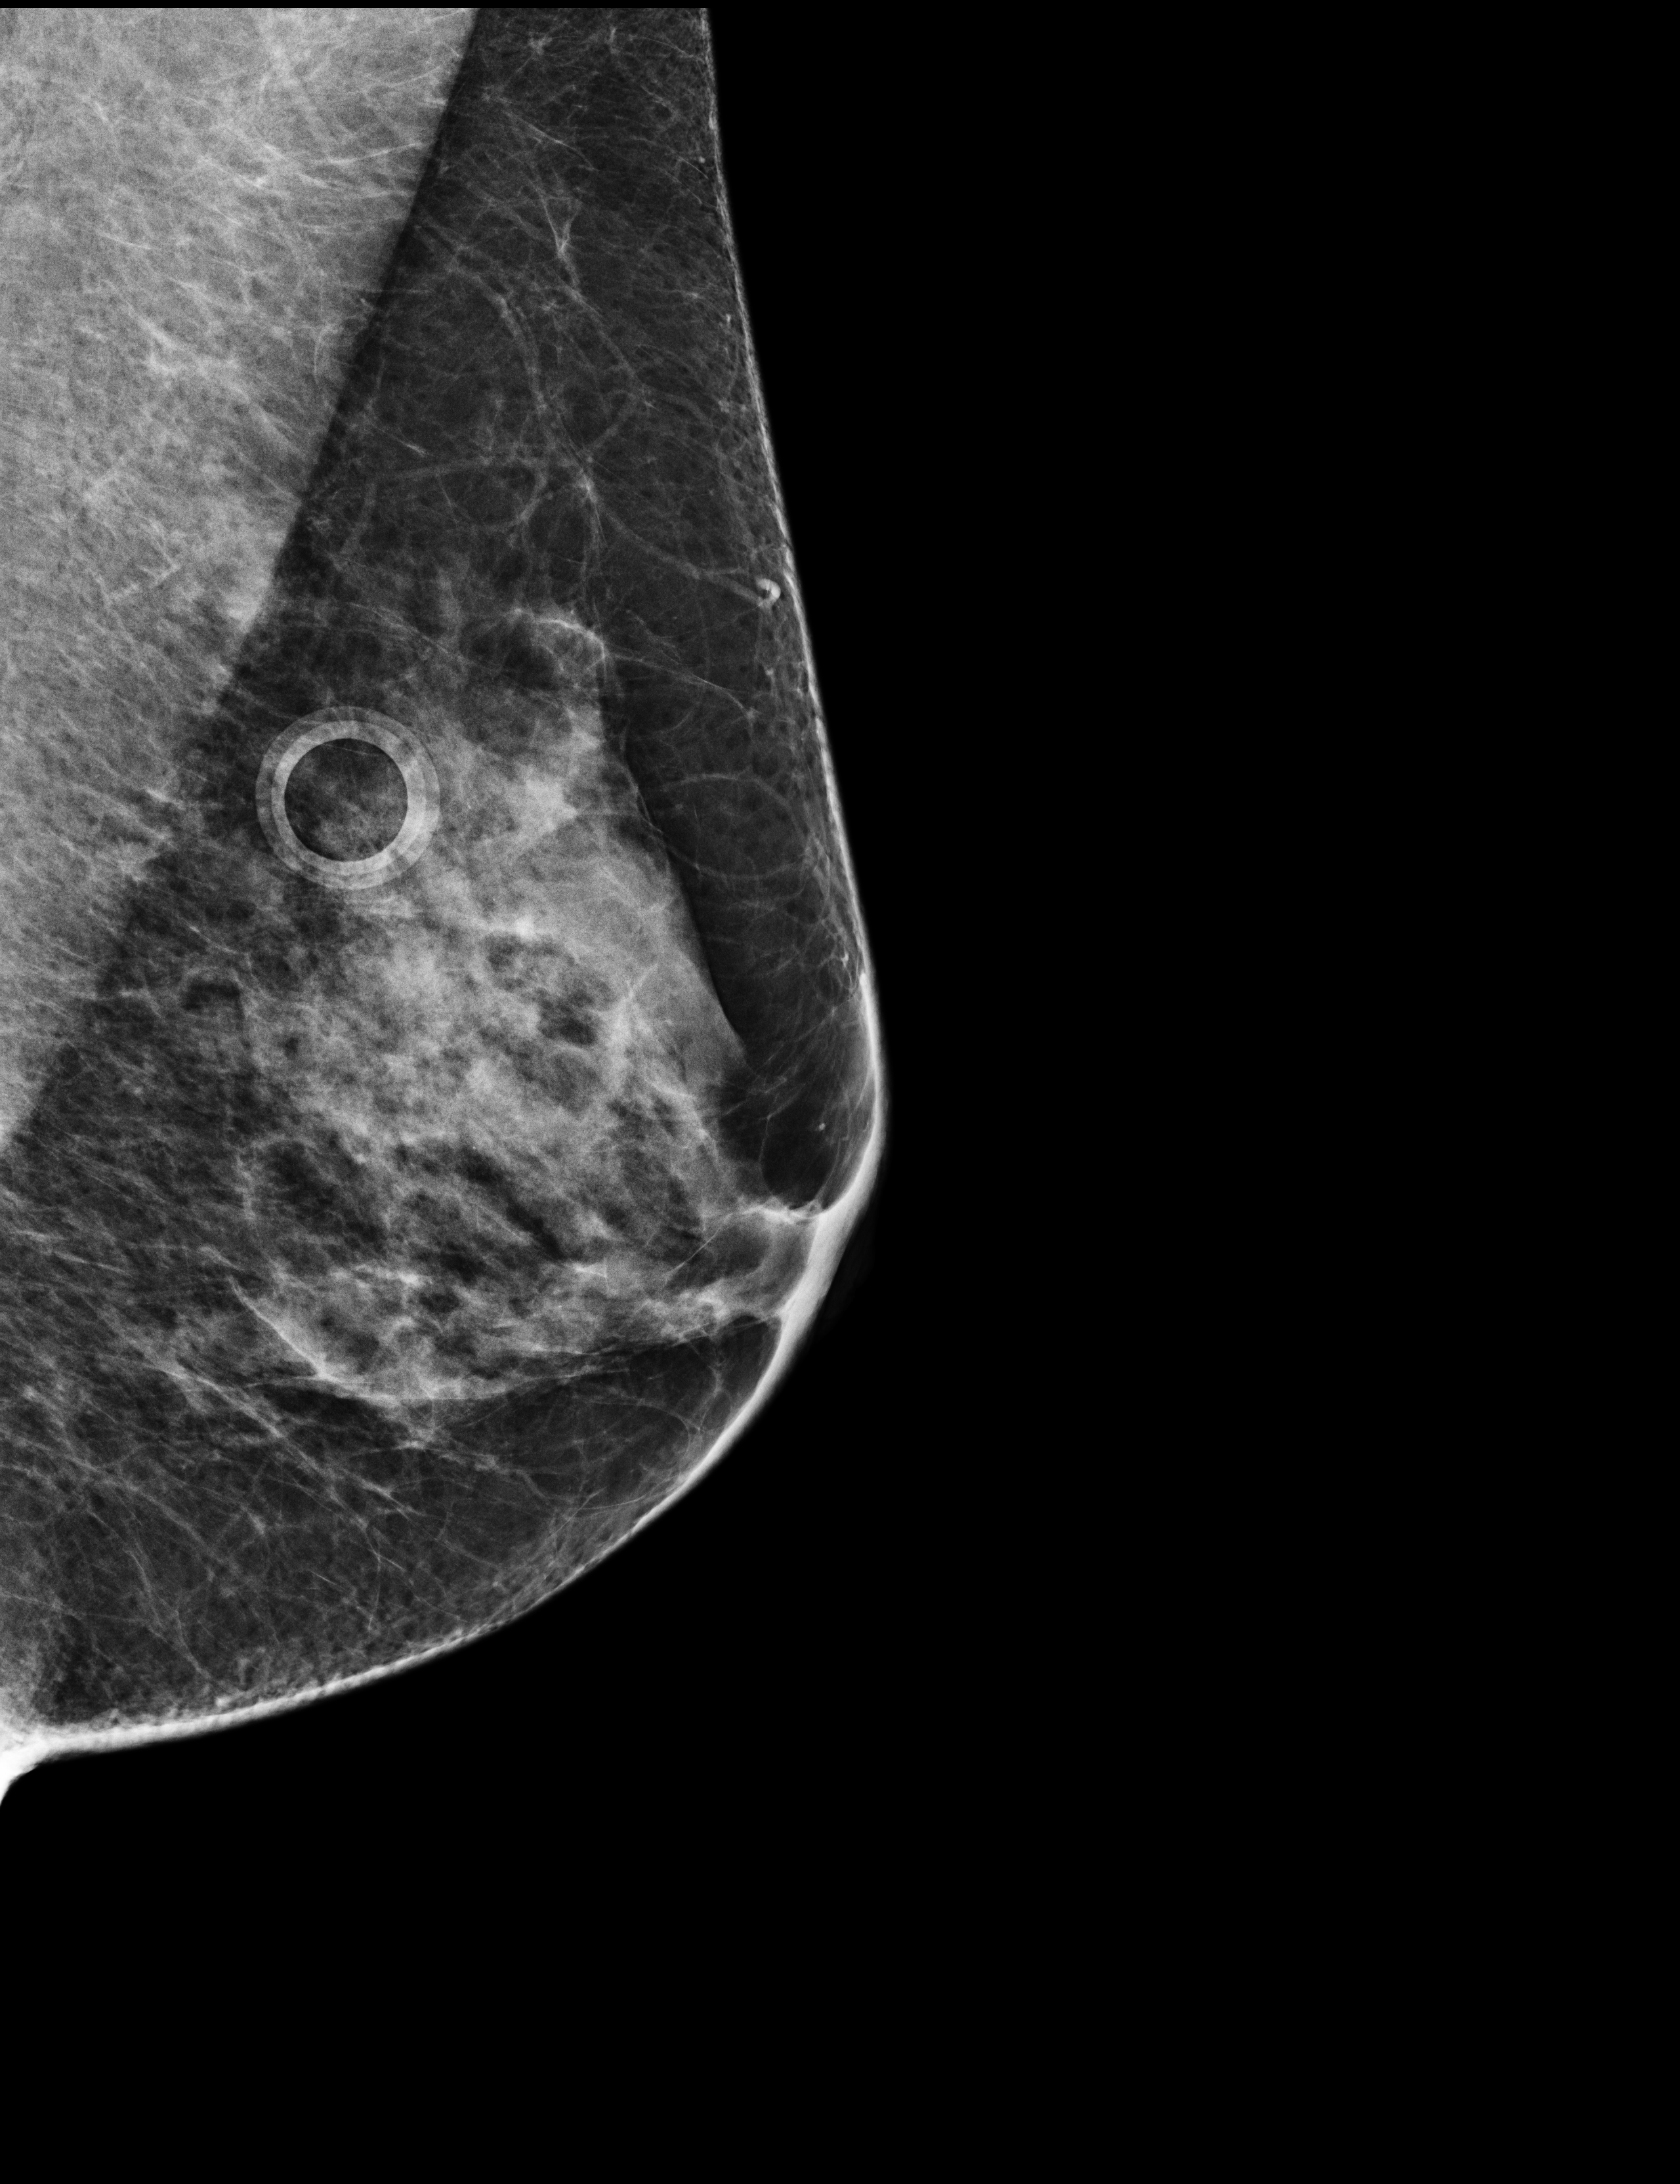
Digital mammogram (FFDM); left breast; medio-lateral oblique projection; annual screening mammography examination. Female patient, age 58 years.
BI-RADS breast density category at the screening exam (both breasts, scale 1–4): 3. Final BI-RADS category for the screening round (tomosynthesis exam, both breasts): category 4. Recall: recalled for additional imaging after this screen.